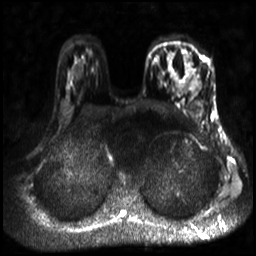
Breast MRI, one axial slice; slice 22 of 30 in the series (ordered by position); diffusion-weighted series; image 2 of 4 stored at this slice position (different b-values; order by instance number); 3 T; 256 × 256 image matrix, field of view 320 × 320 mm. Female patient.
Outlined on this slice (manually delineated by an expert):
- tumour on diffusion-weighted imaging: bounding box (x1, y1, x2, y2) in pixels: (190, 79, 197, 91)